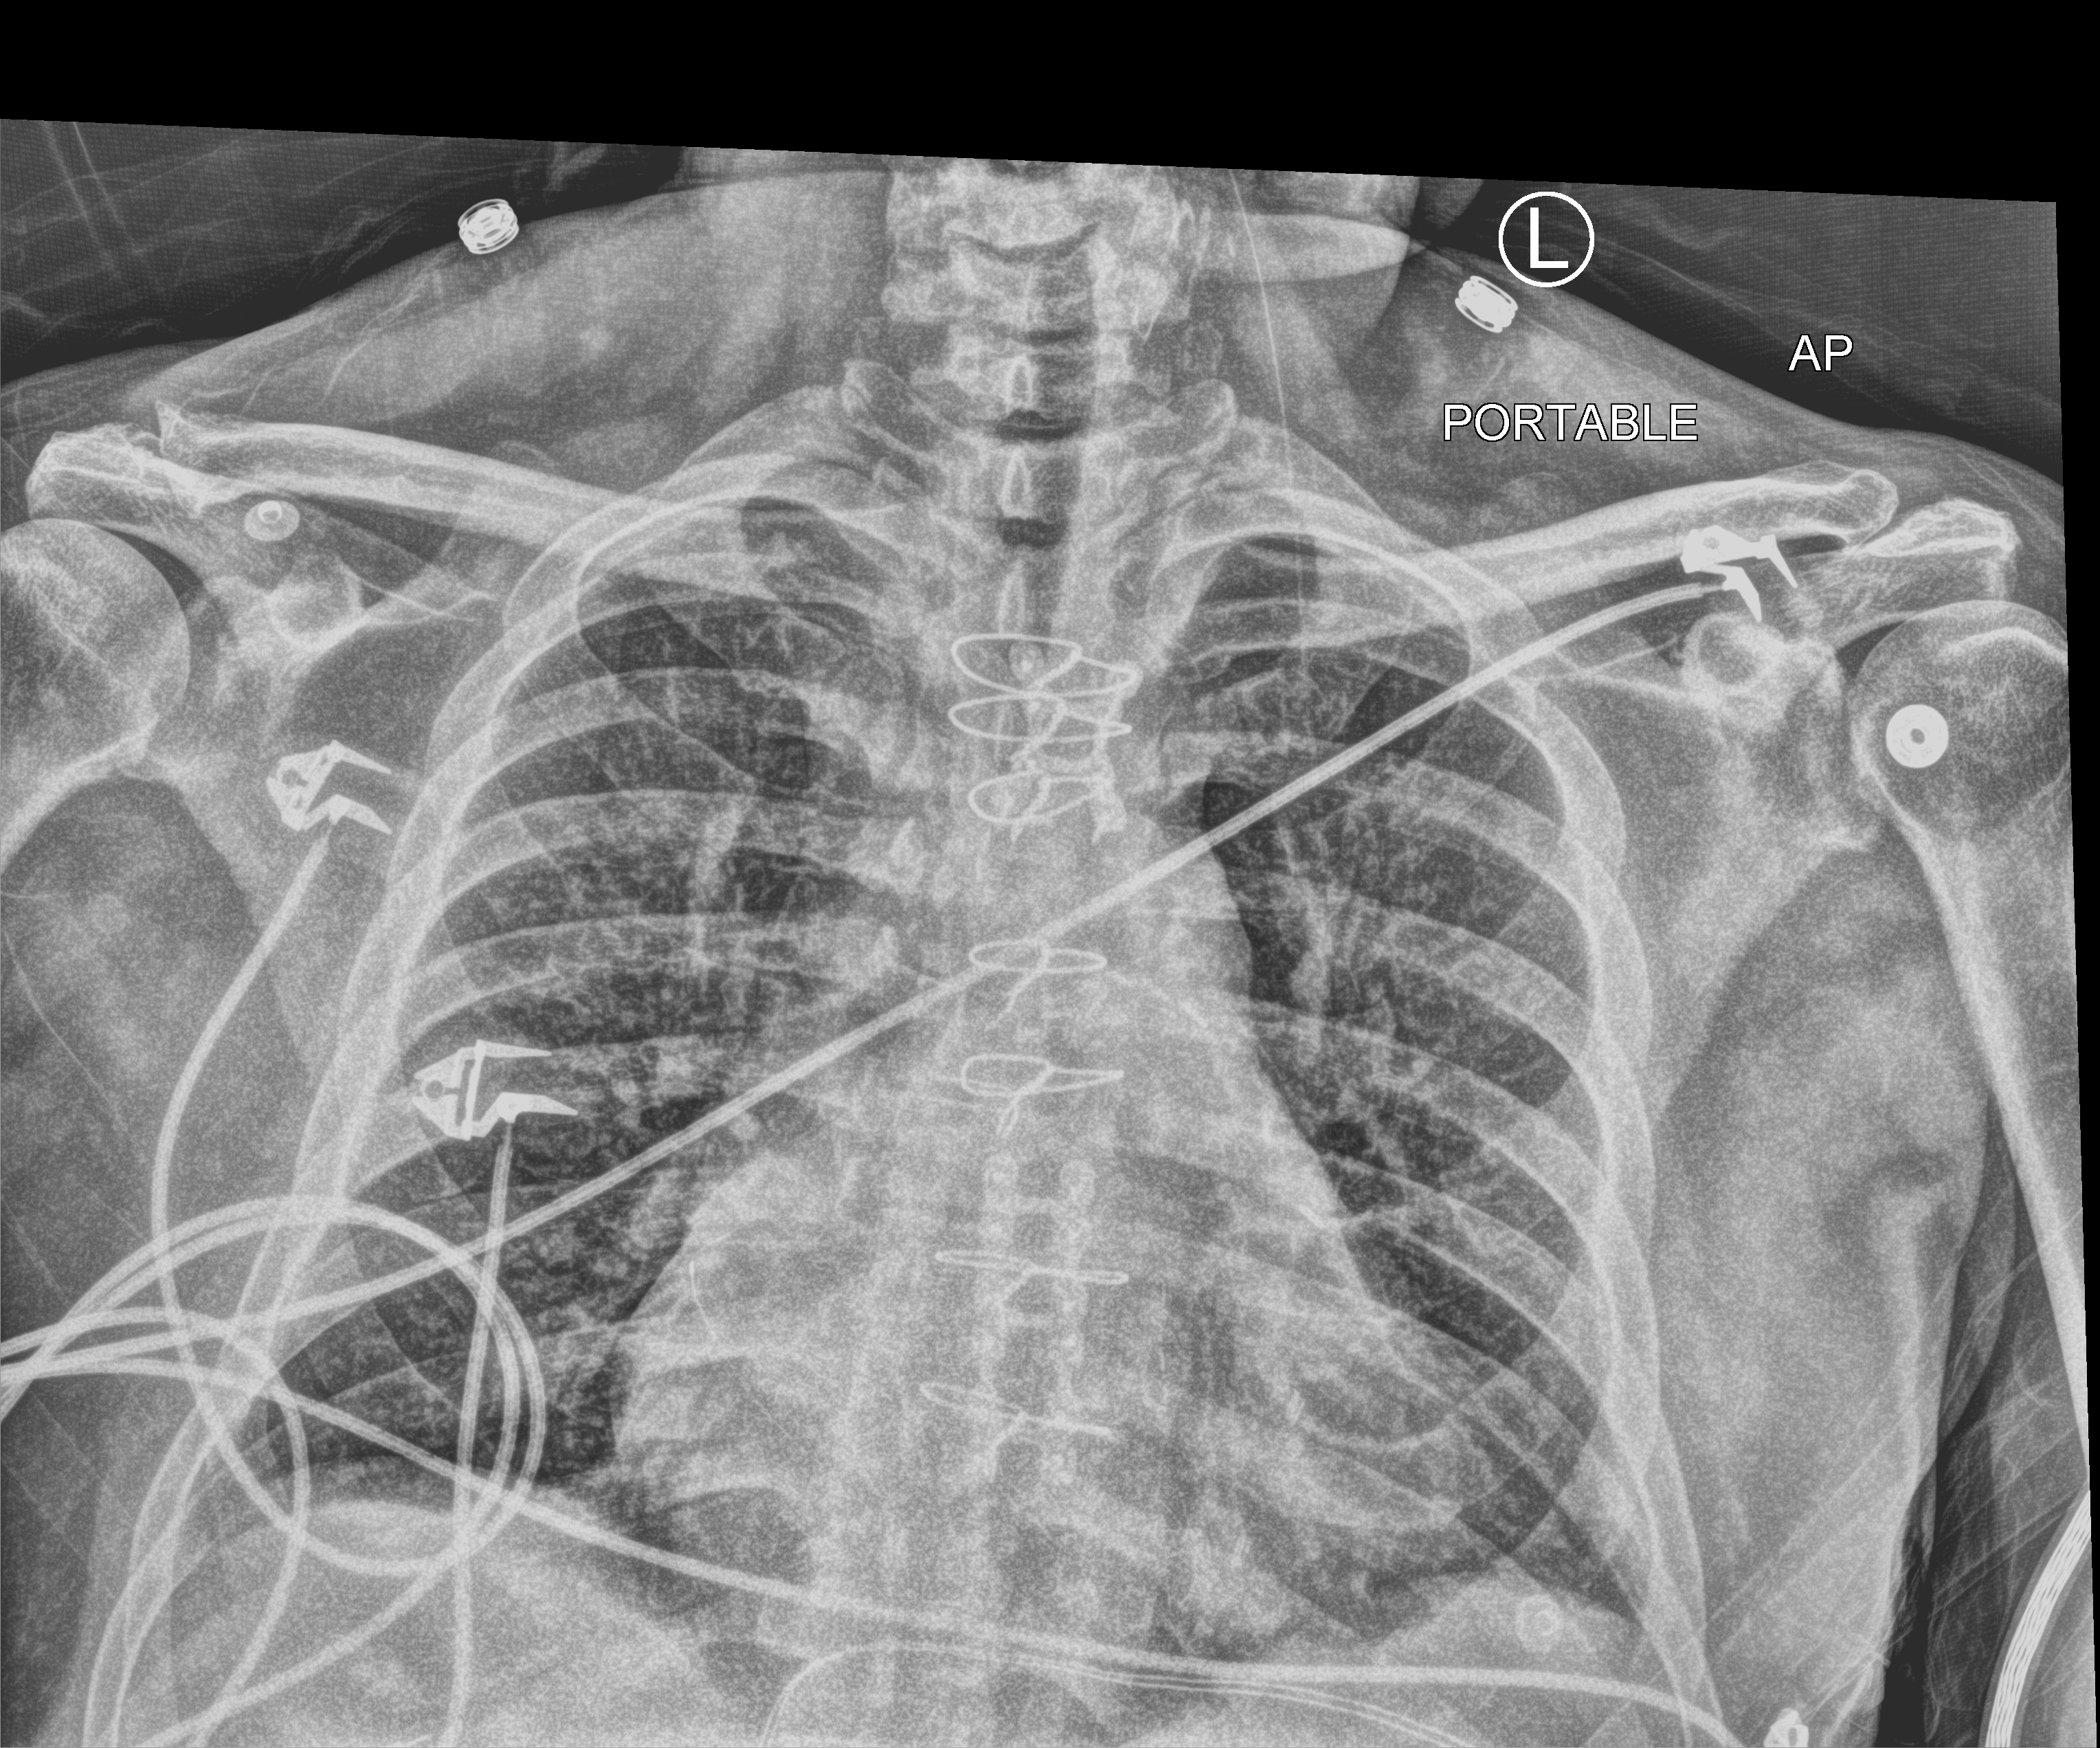
Portable chest radiograph; anteroposterior (AP) projection. Patient hospitalised with COVID-19; male, aged 60–74 years.
From the hospital-stay record, not from the radiograph (when in the stay this image was taken is not recorded):
- mechanically ventilated during this hospital stay: no
- hypertension (admission record): yes
- admitted to intensive care during this hospital stay: no